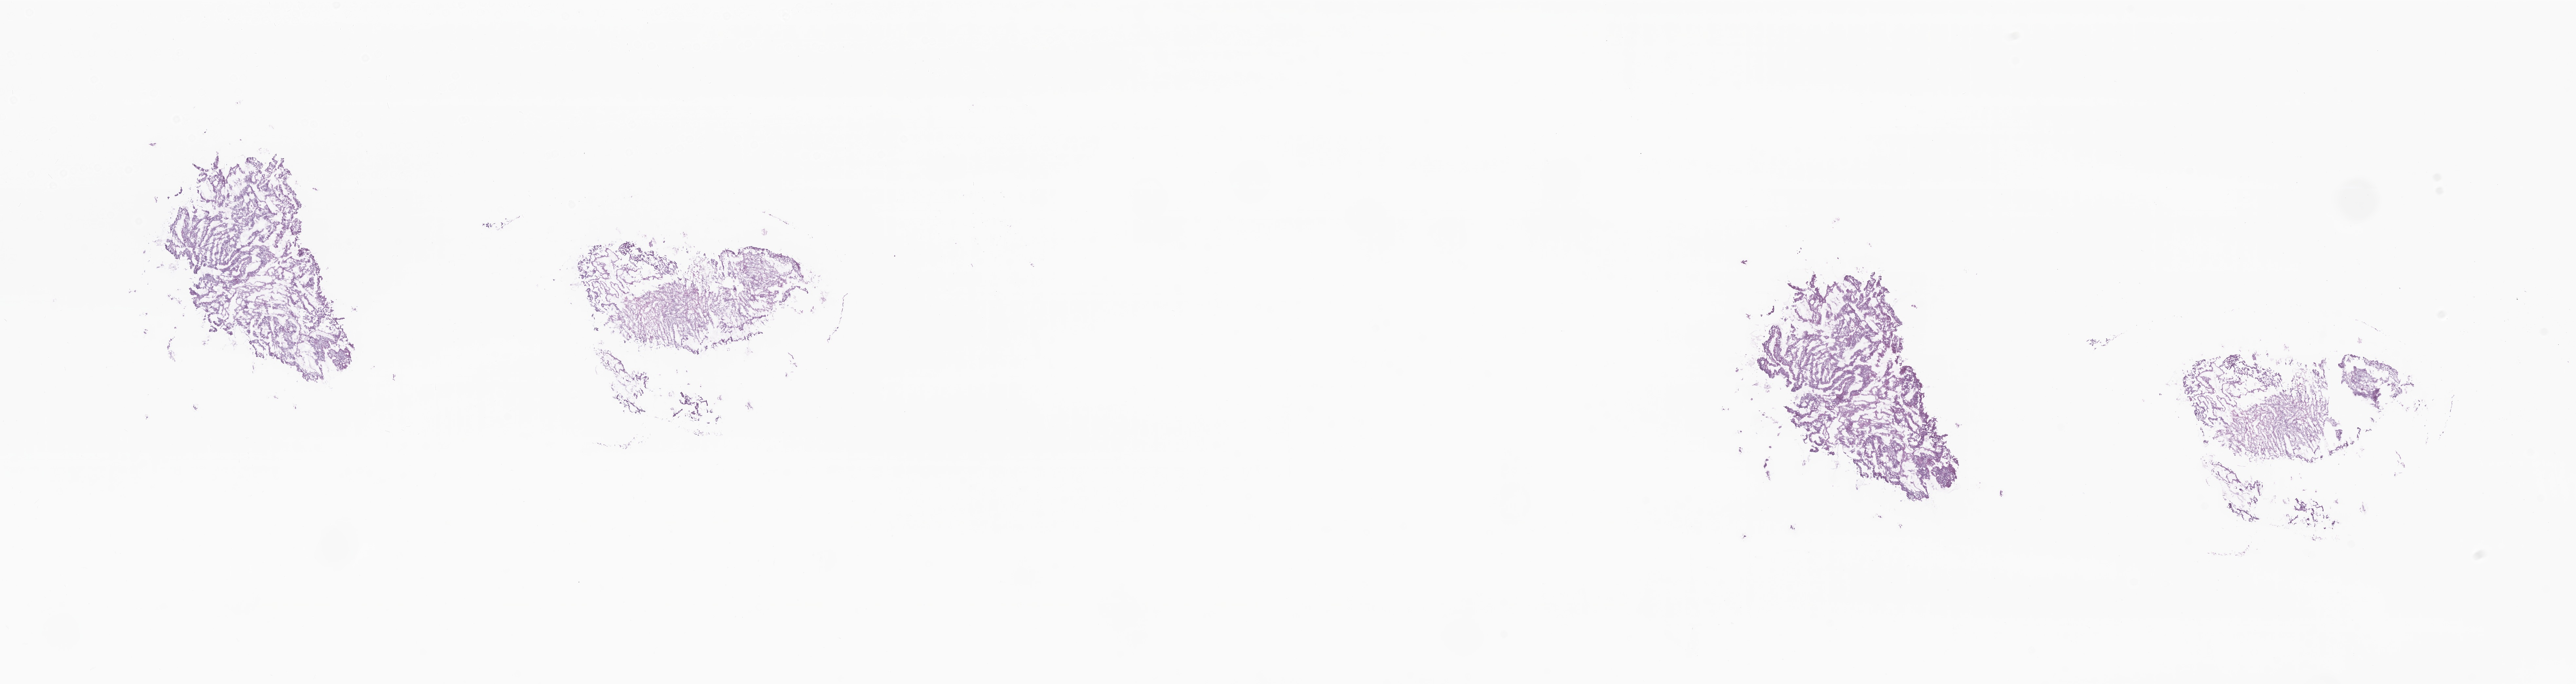
Digitized H&E-stained section — a low-resolution overview of the entire scanned area, about 33.2 x 8.8 mm. Frozen section (tissue freezing medium). Primary tumor. Site: sigmoid colon. Male patient; age at initial diagnosis 66 years. Pathologist review of this section (percent, as recorded): tumor cells 80%, tumor nuclei 80%, stromal cells 20%, necrosis 0%, normal cells 0%. Inflammatory infiltration, as recorded: lymphocyte infiltration 4%, monocyte infiltration 2%, neutrophil infiltration 6%.
Diagnosis: Adenocarcinoma, NOS.